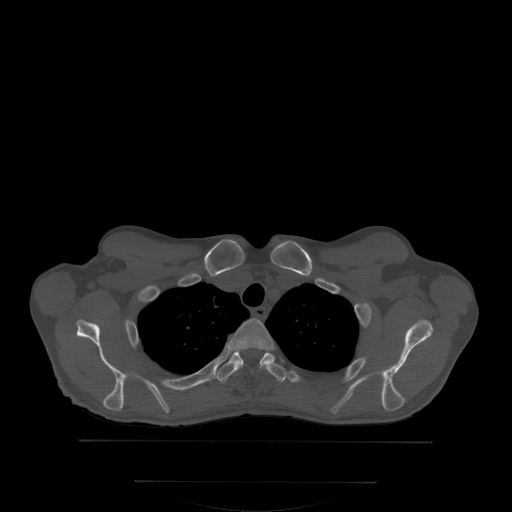
CT including the spine, one axial slice. Slice 273 of 350 in the series (ordered by position). Bone window (W 1800 / L 400 HU). 2.5 mm slice thickness. 512 × 512 image matrix. Patient: male, 58 years. Case-level facts recorded for this patient, not image findings: primary cancer: prostate; vertebrae with lytic lesions (as recorded): L1.
Outlined on this slice (semi-automatic segmentation, software-assisted and operator-edited):
- T2 vertebra: bounding box (x1, y1, x2, y2) in pixels: (230, 318, 275, 350)
- T3 vertebra: (216, 345, 287, 382)